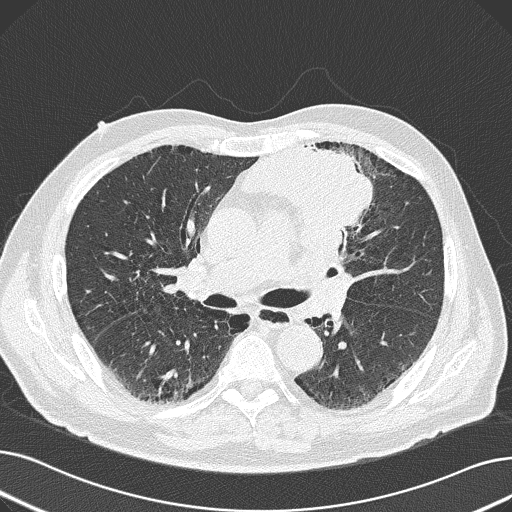
Axial slice from a low-dose chest CT screening exam. Baseline annual screen. Lung window (W 1500 / L -600 HU). Lung (sharp) reconstruction kernel (B50f). 512 × 512 image matrix, field of view 370 × 370 mm. Male, age 69 years at enrolment.
- Lesion marked by an expert reader, box from (x=237, y=131) to (x=385, y=249) px.
- The exam's reader record, not a measurement of the box and not confirmed to be the same lesion: non-calcified nodule or mass ≥4 mm, left upper lobe, 6 × 10 mm, spiculated (stellate) margins, soft tissue attenuation.
- Later outcome: lung cancer diagnosed 20 days after this screen — non-small cell carcinoma, left upper lobe, poorly differentiated (G3), stage IB (AJCC 6th edition), 100 mm at pathology.